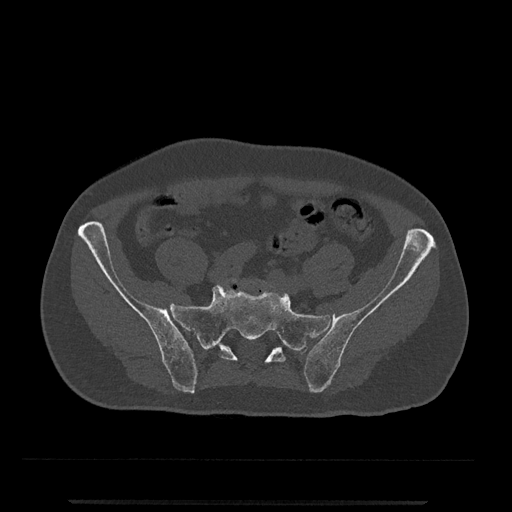
CT including the spine, one axial slice. Slice 11 of 797 in the series (ordered by position). Reconstruction kernel Br40s/3. 120 kVp. Bone window (W 1800 / L 400 HU). 512 × 512 image matrix, field of view 419 × 419 mm. Male patient, age 63 years. From the clinical record (not read from this slice): primary cancer: prostate.
Annotated regions visible in this slice (semi-automatic segmentation, software-assisted and operator-edited):
- L5 vertebra: bounding box (x1, y1, x2, y2) in pixels: (230, 278, 255, 283)